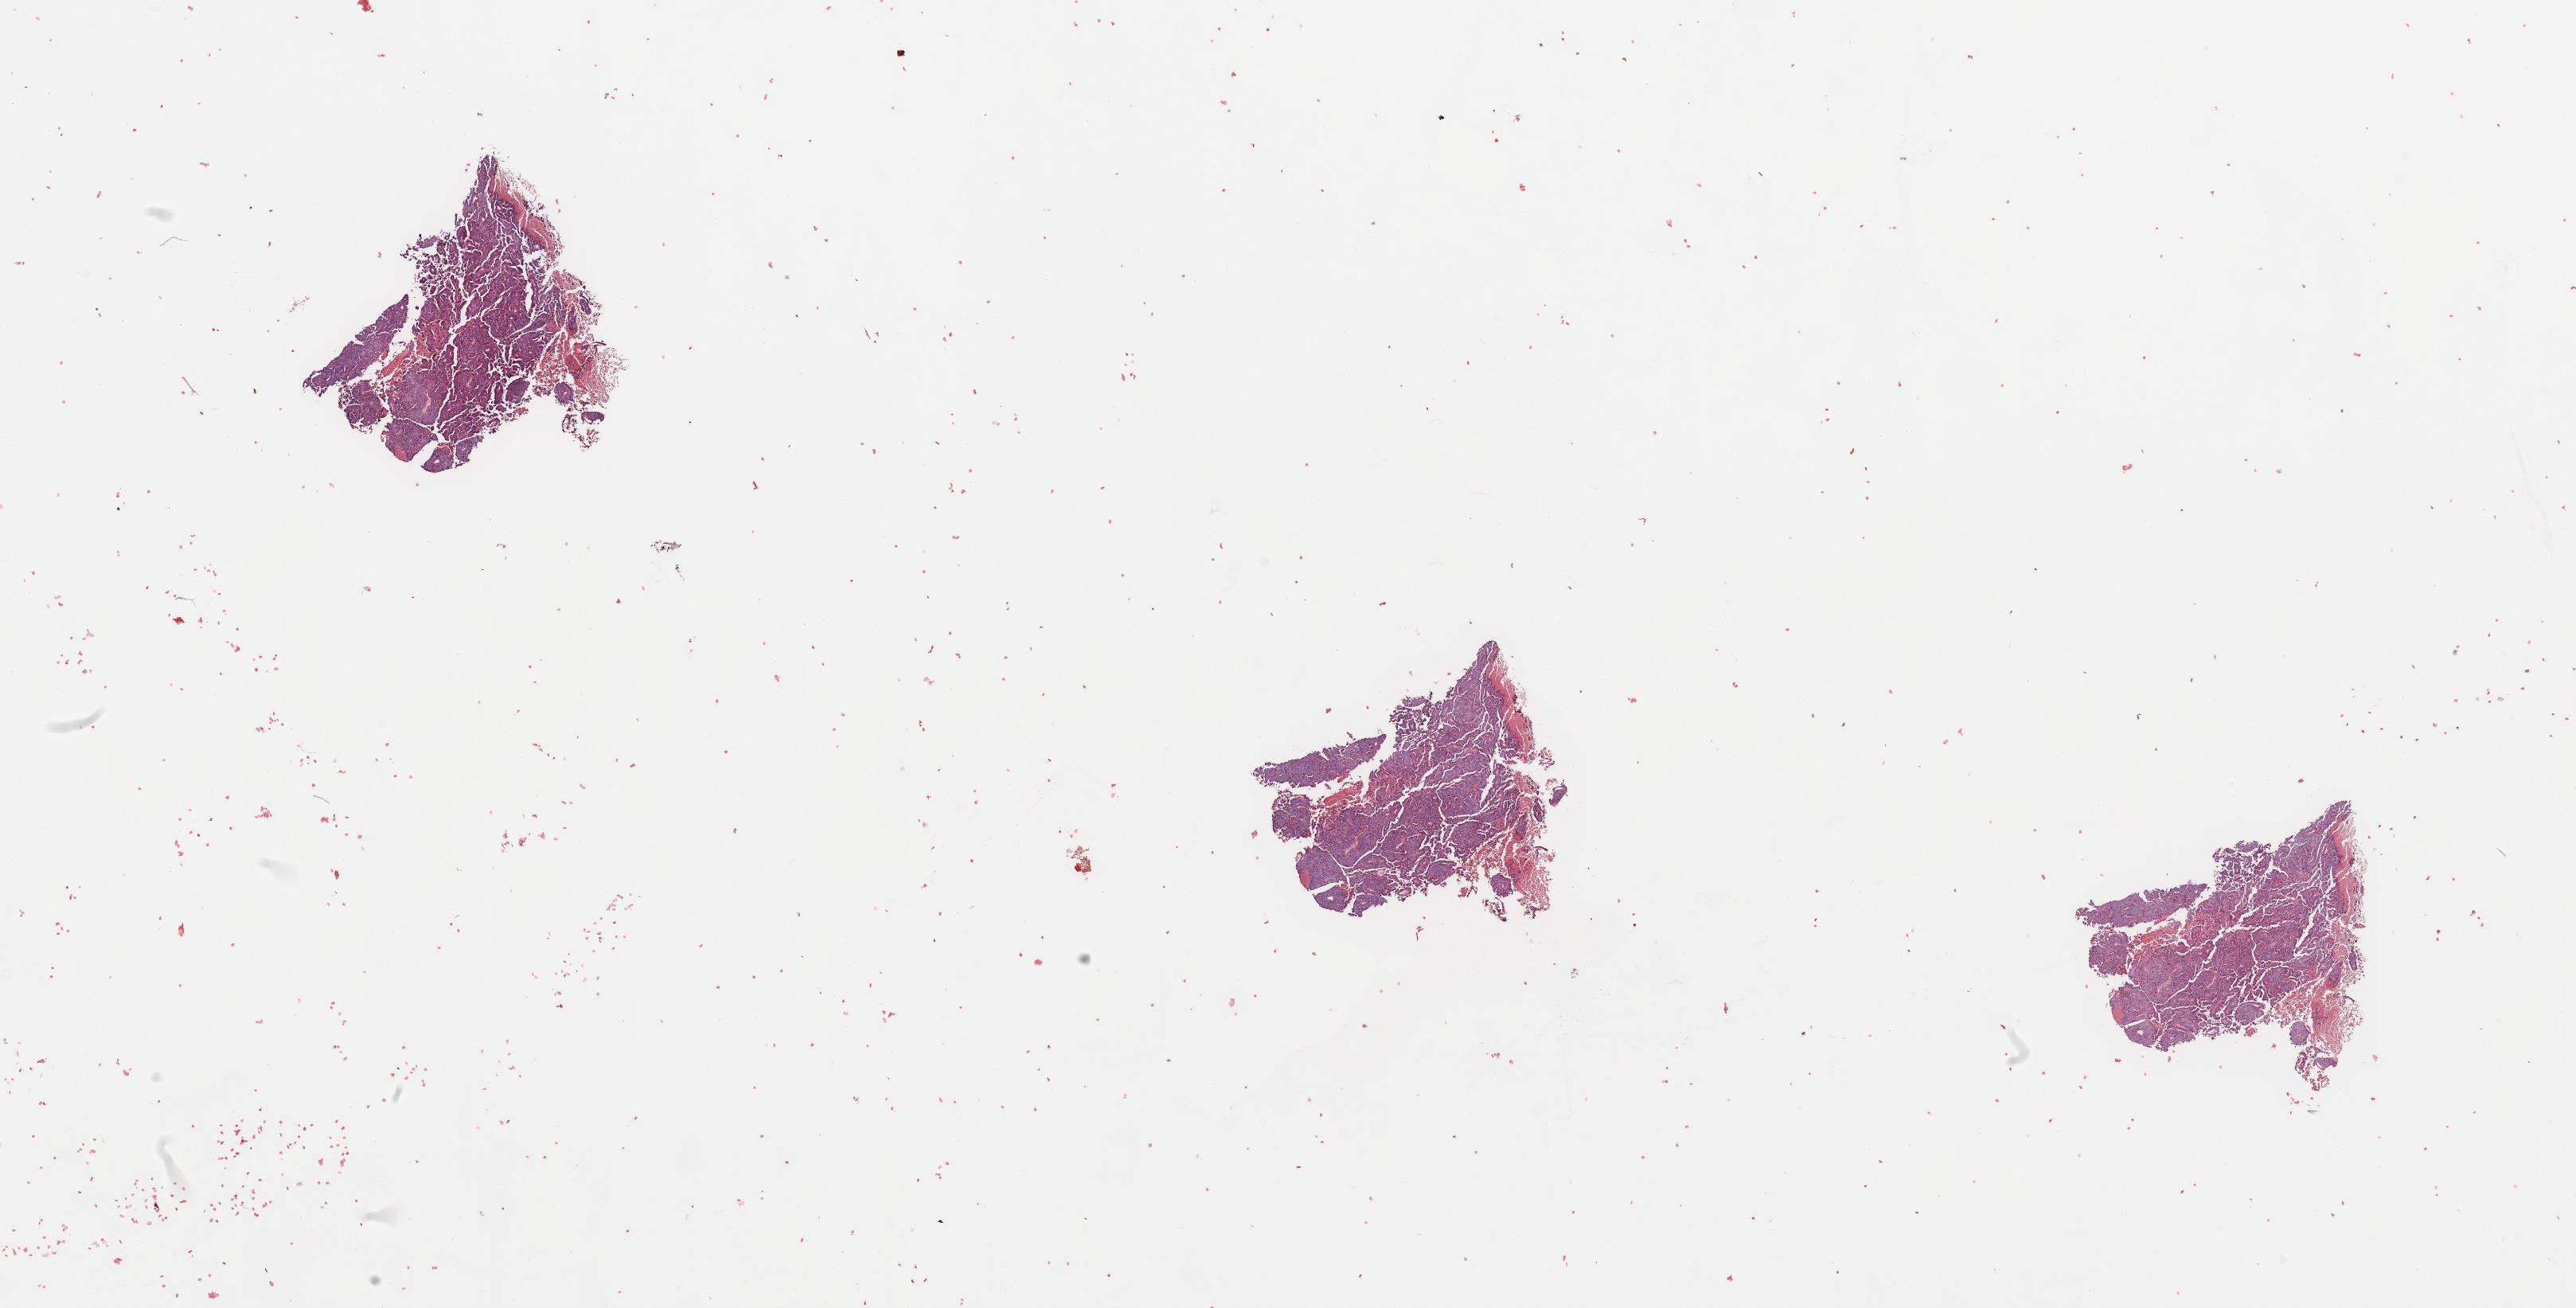
H&E whole-slide image — whole scanned area (about 25.6 x 13.0 mm) shown as a low-resolution overview. Uterus, tumour tissue. 73-year-old female patient.
Histologic diagnosis: Endometrioid adenocarcinoma, NOS.